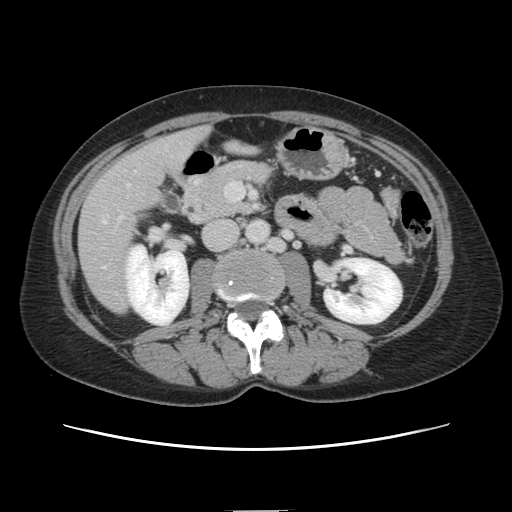
Contrast-enhanced abdominal CT, one axial slice. Position 47 of 141 along the scan axis. Intravenous contrast given. Soft-tissue window (W 400 / L 40 HU). 2.5 mm slice thickness. 512 × 512 image matrix, field of view 350 × 350 mm. Female patient, age 63 years. From the clinical record (not read from this slice): diagnosis: colorectal cancer liver metastases, imaged before liver resection; multiple liver metastases: yes; largest metastasis: 3.2 cm; chemotherapy before resection: yes.
Annotated regions visible in this slice (expert manual segmentation):
- liver: box from (x=80, y=130) to (x=206, y=312) px
- planned liver remnant (the part of the liver to remain after resection): (x=180, y=129)–(x=206, y=160)
- portal vein (with intrahepatic branches): (x=103, y=220)–(x=105, y=222)